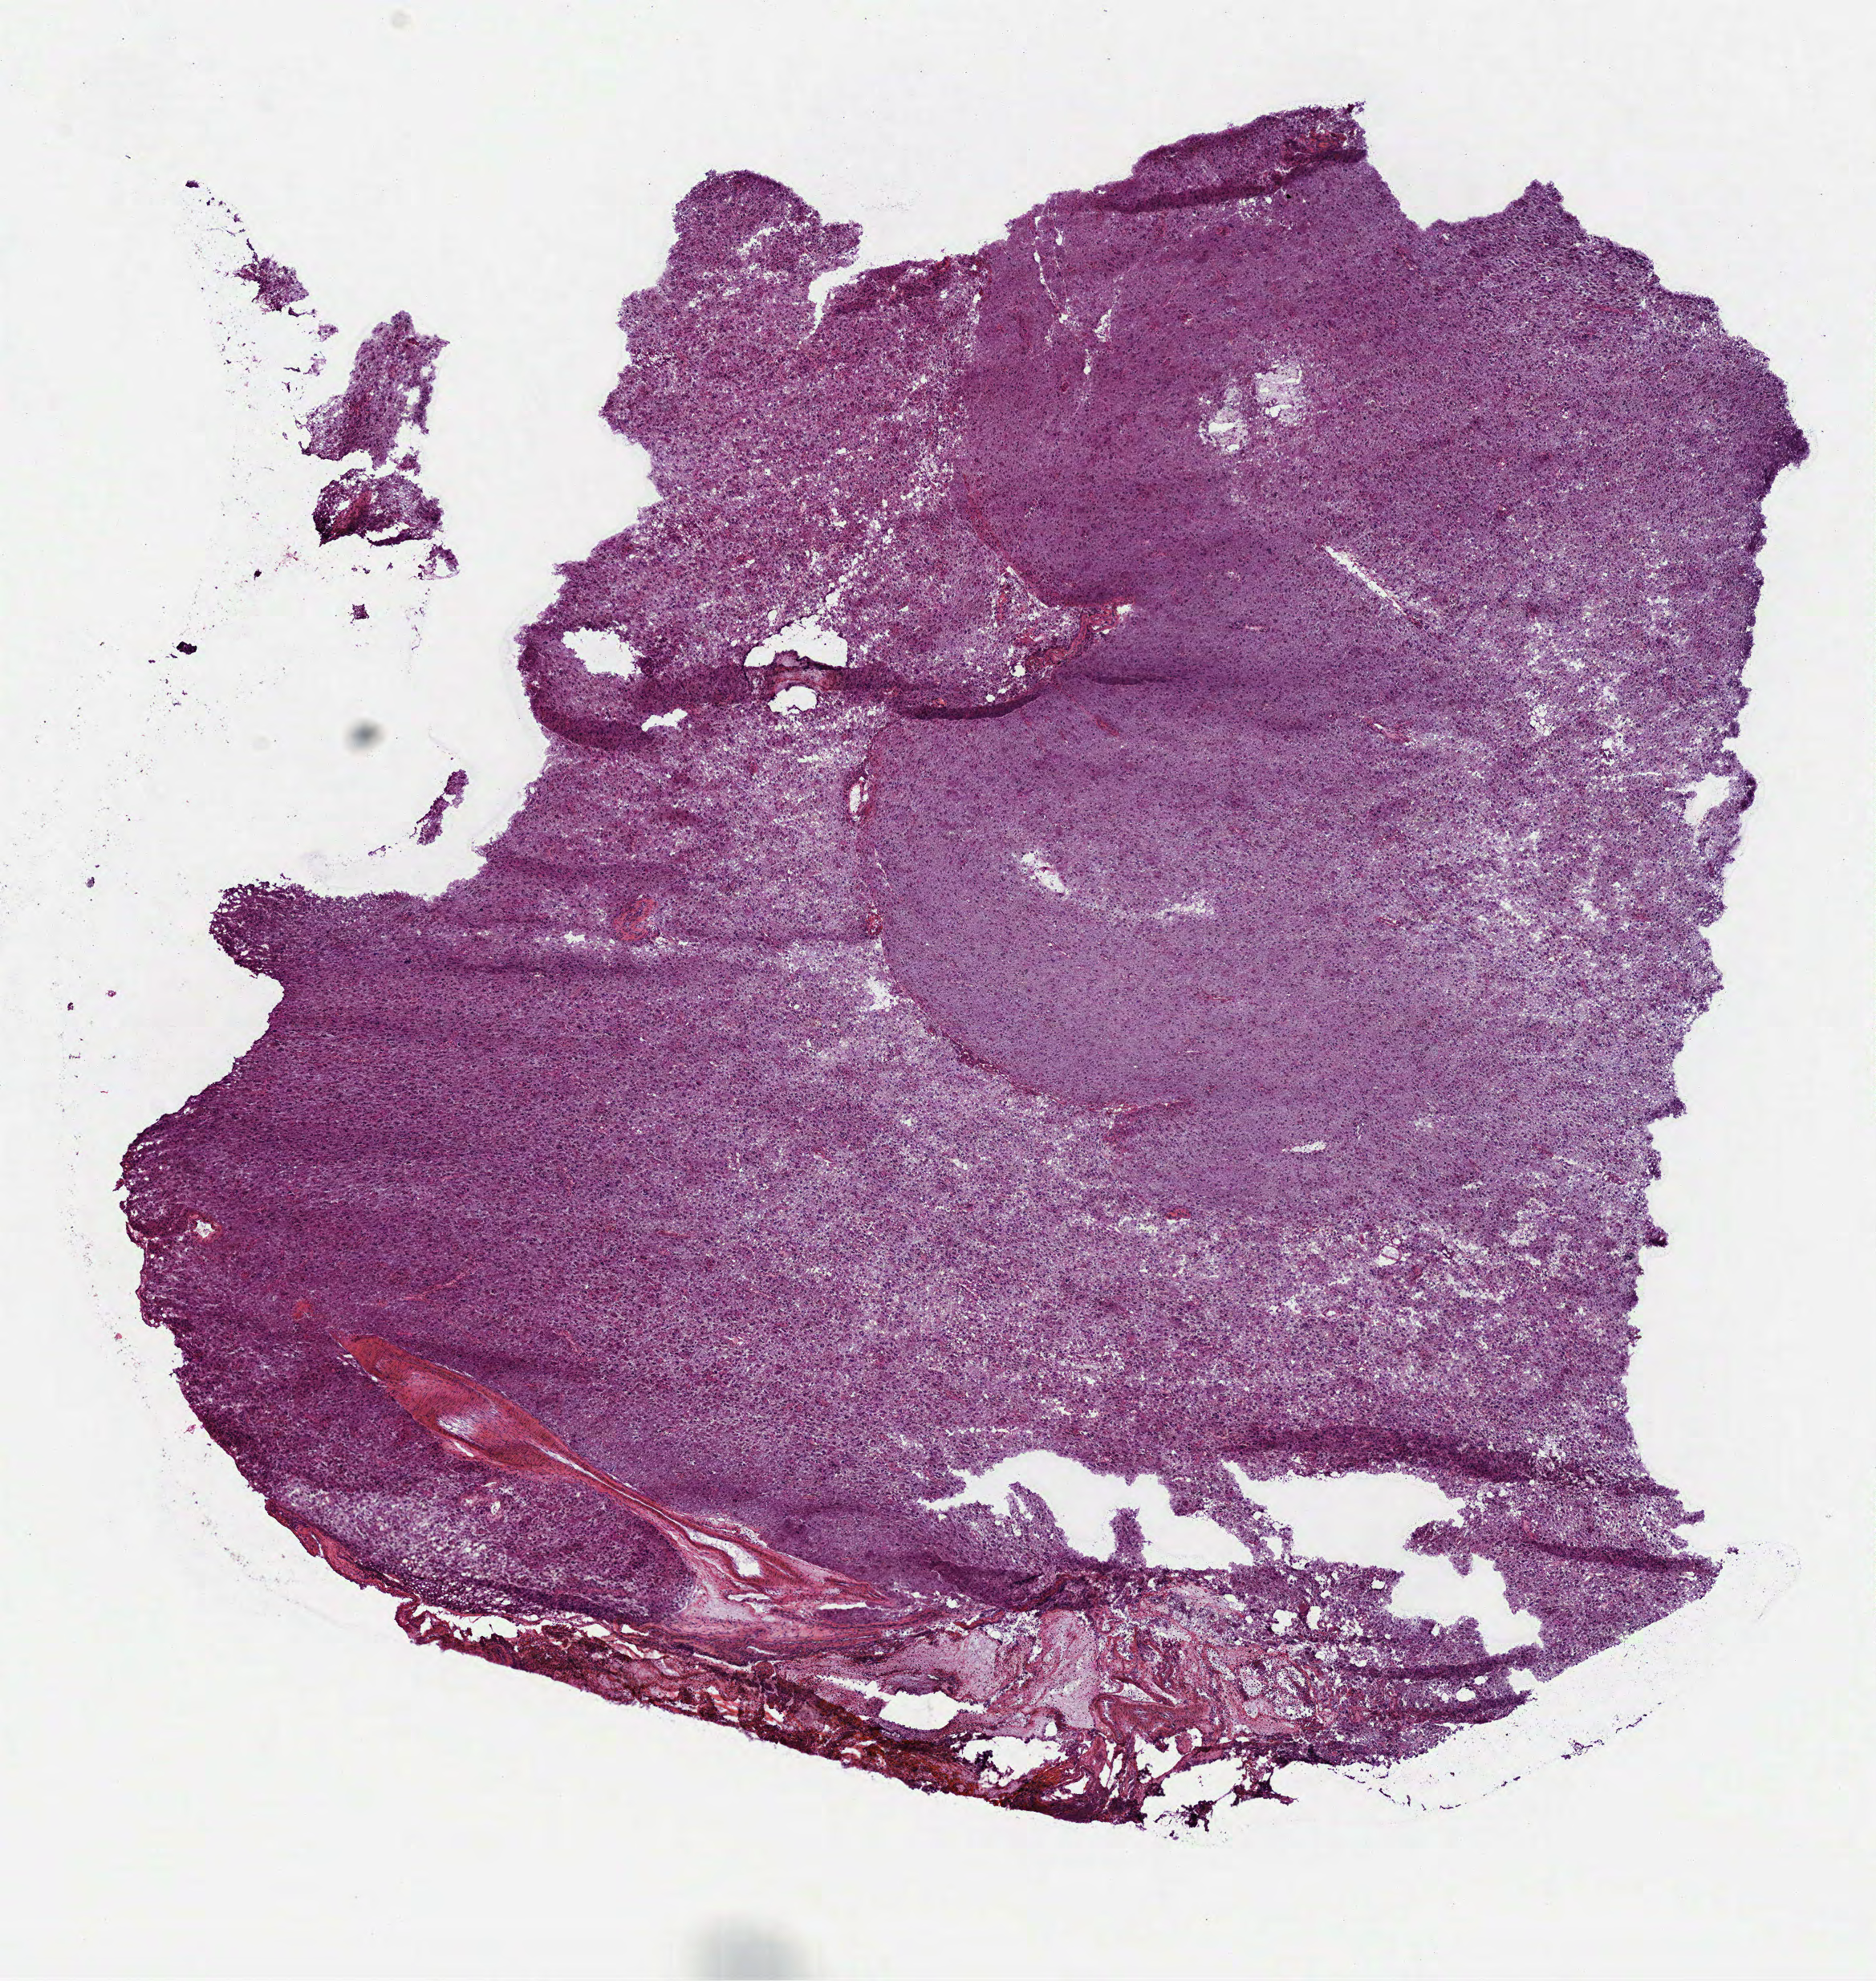
Whole-slide histology image, H&E — a low-resolution overview of the entire scanned area, about 9.4 x 10.0 mm (acquisition: 40x scan), frozen section from the top of the tissue portion, primary tumour sample from the brain. Patient: male, age at initial diagnosis 39 years. Pathologist review of this section (percent, as recorded): tumour cells 100%, tumour nuclei 75%, normal cells 0%, stromal cells 0%, necrosis 0%.
* laterality: right
* diagnosis: Mixed glioma (cerebrum)